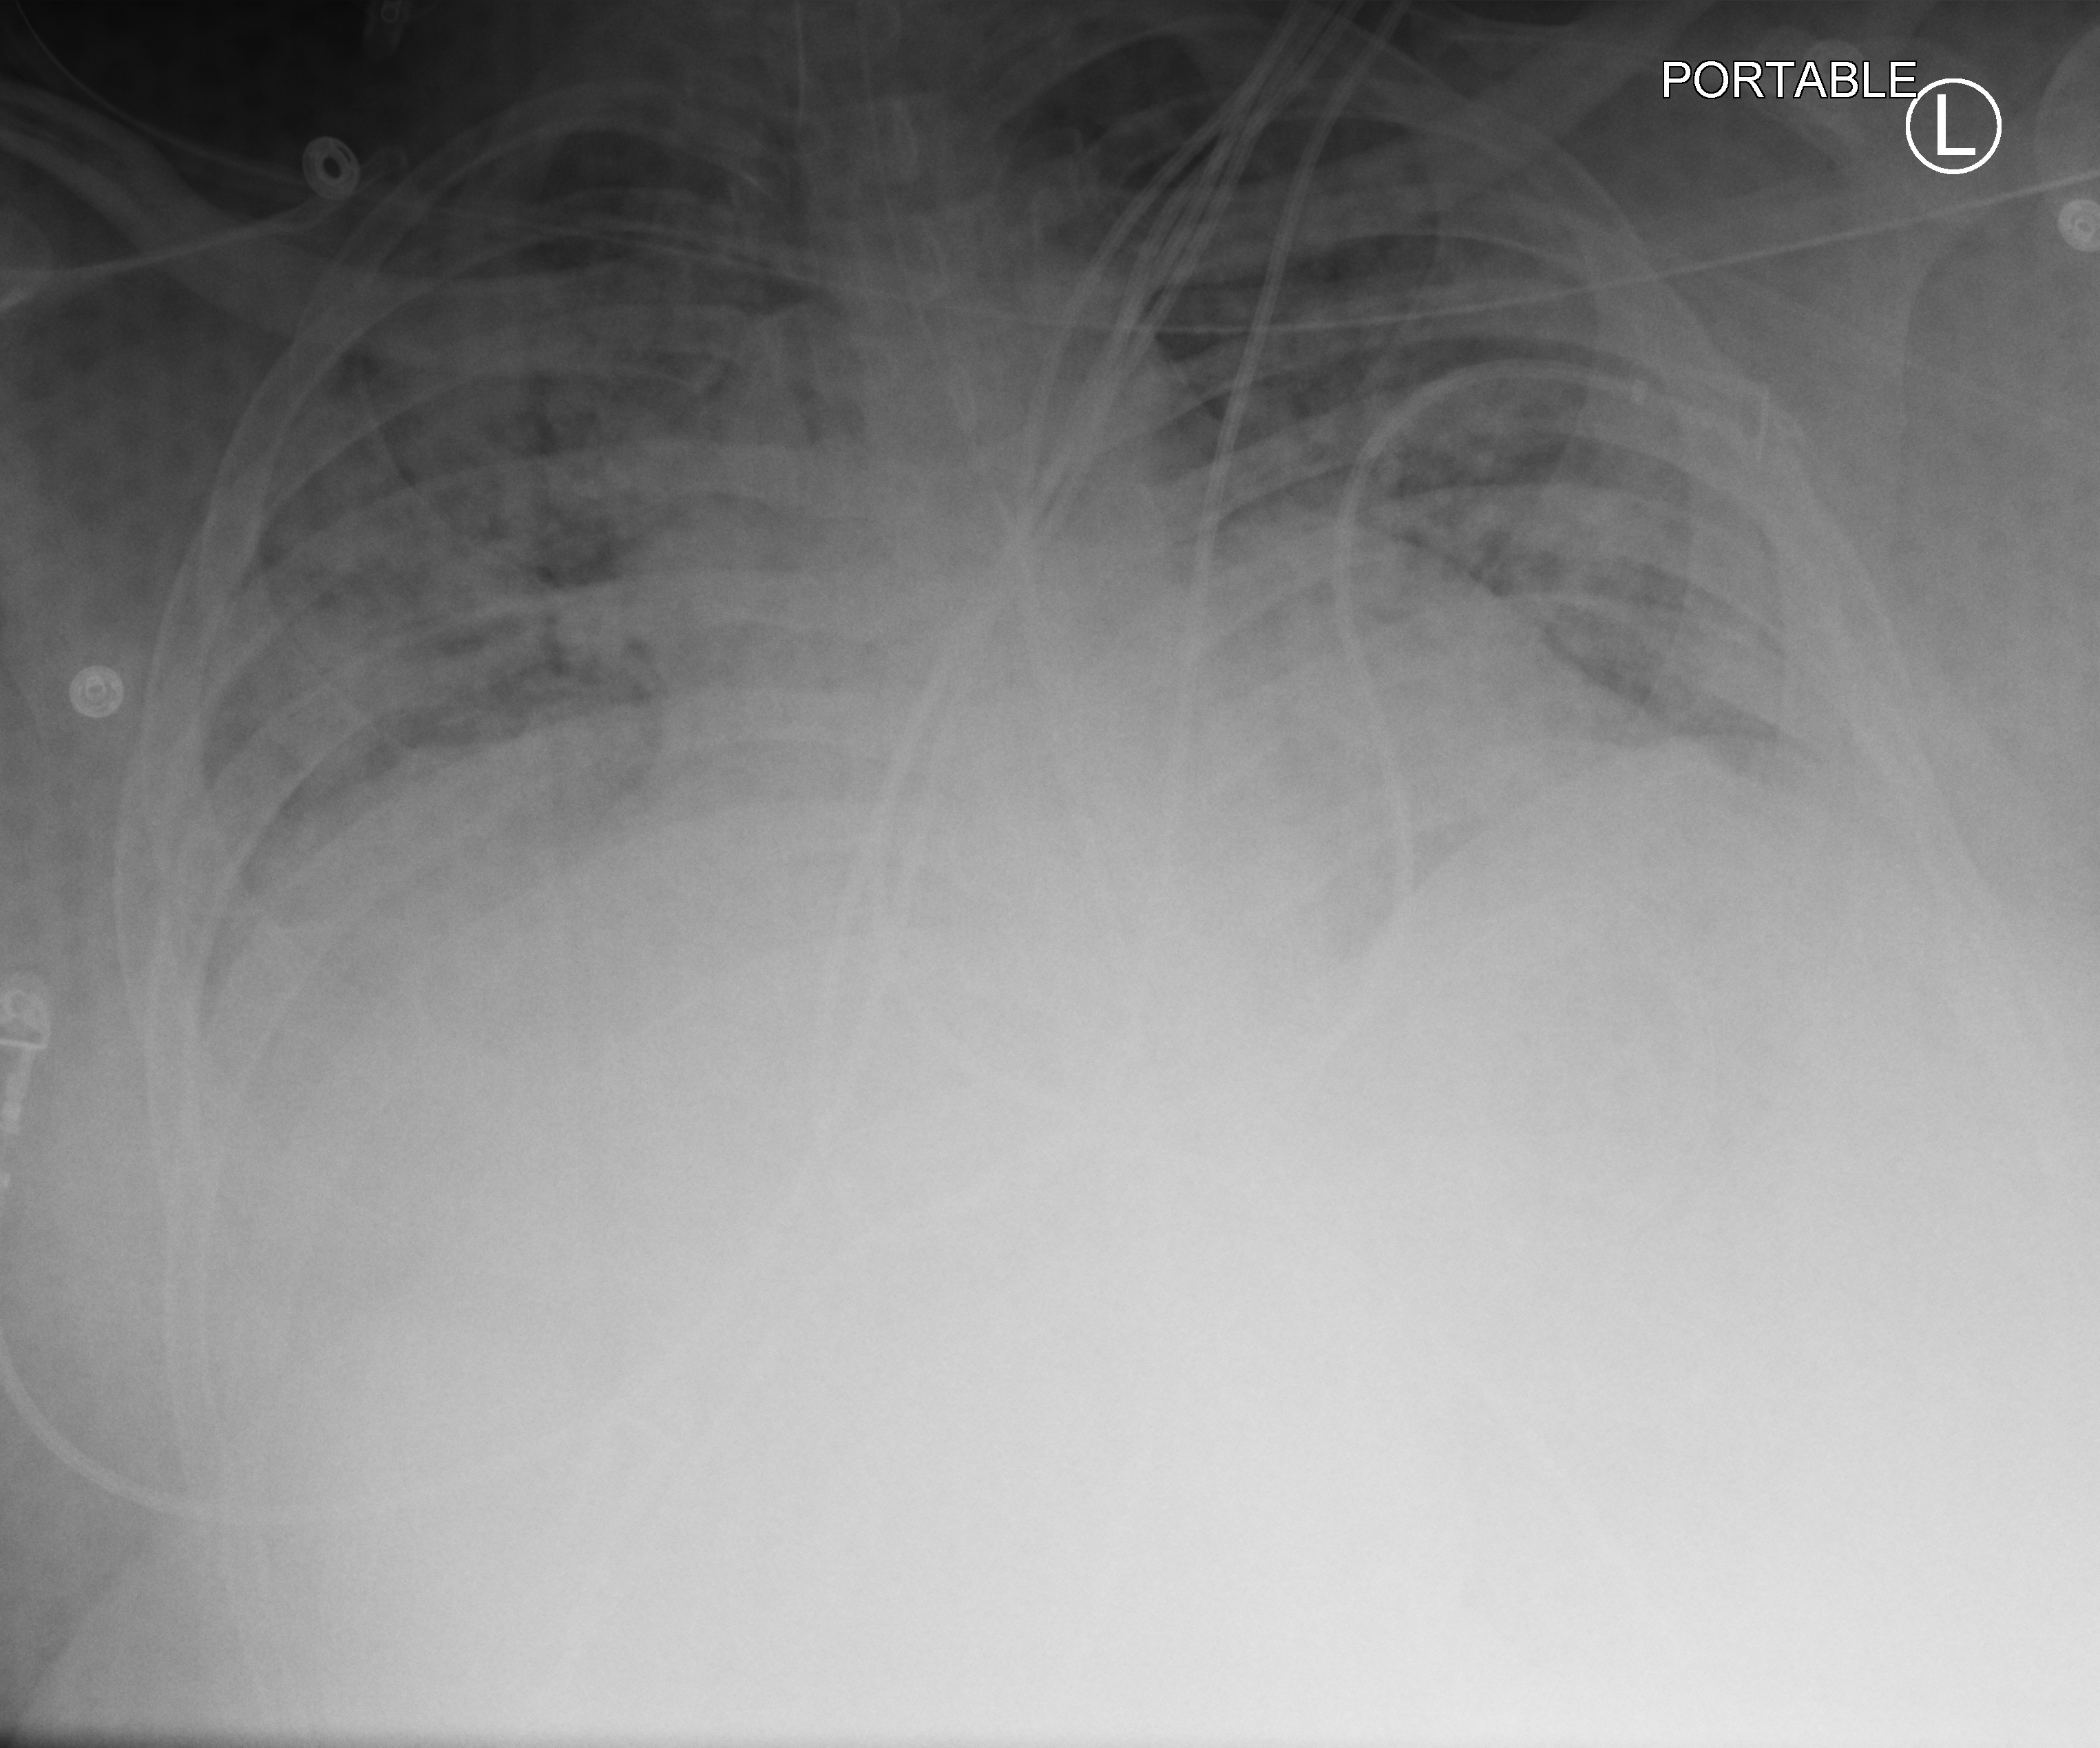
Bedside chest radiograph (computed radiography), anteroposterior (AP) projection. Patient hospitalised with COVID-19; male, aged 18–59 years.
Admission-level facts for this patient (not findings on this image; timing relative to this image not recorded): mechanically ventilated during this hospital stay: yes; length of hospital stay: 69 days; admitted to intensive care during this hospital stay: yes.